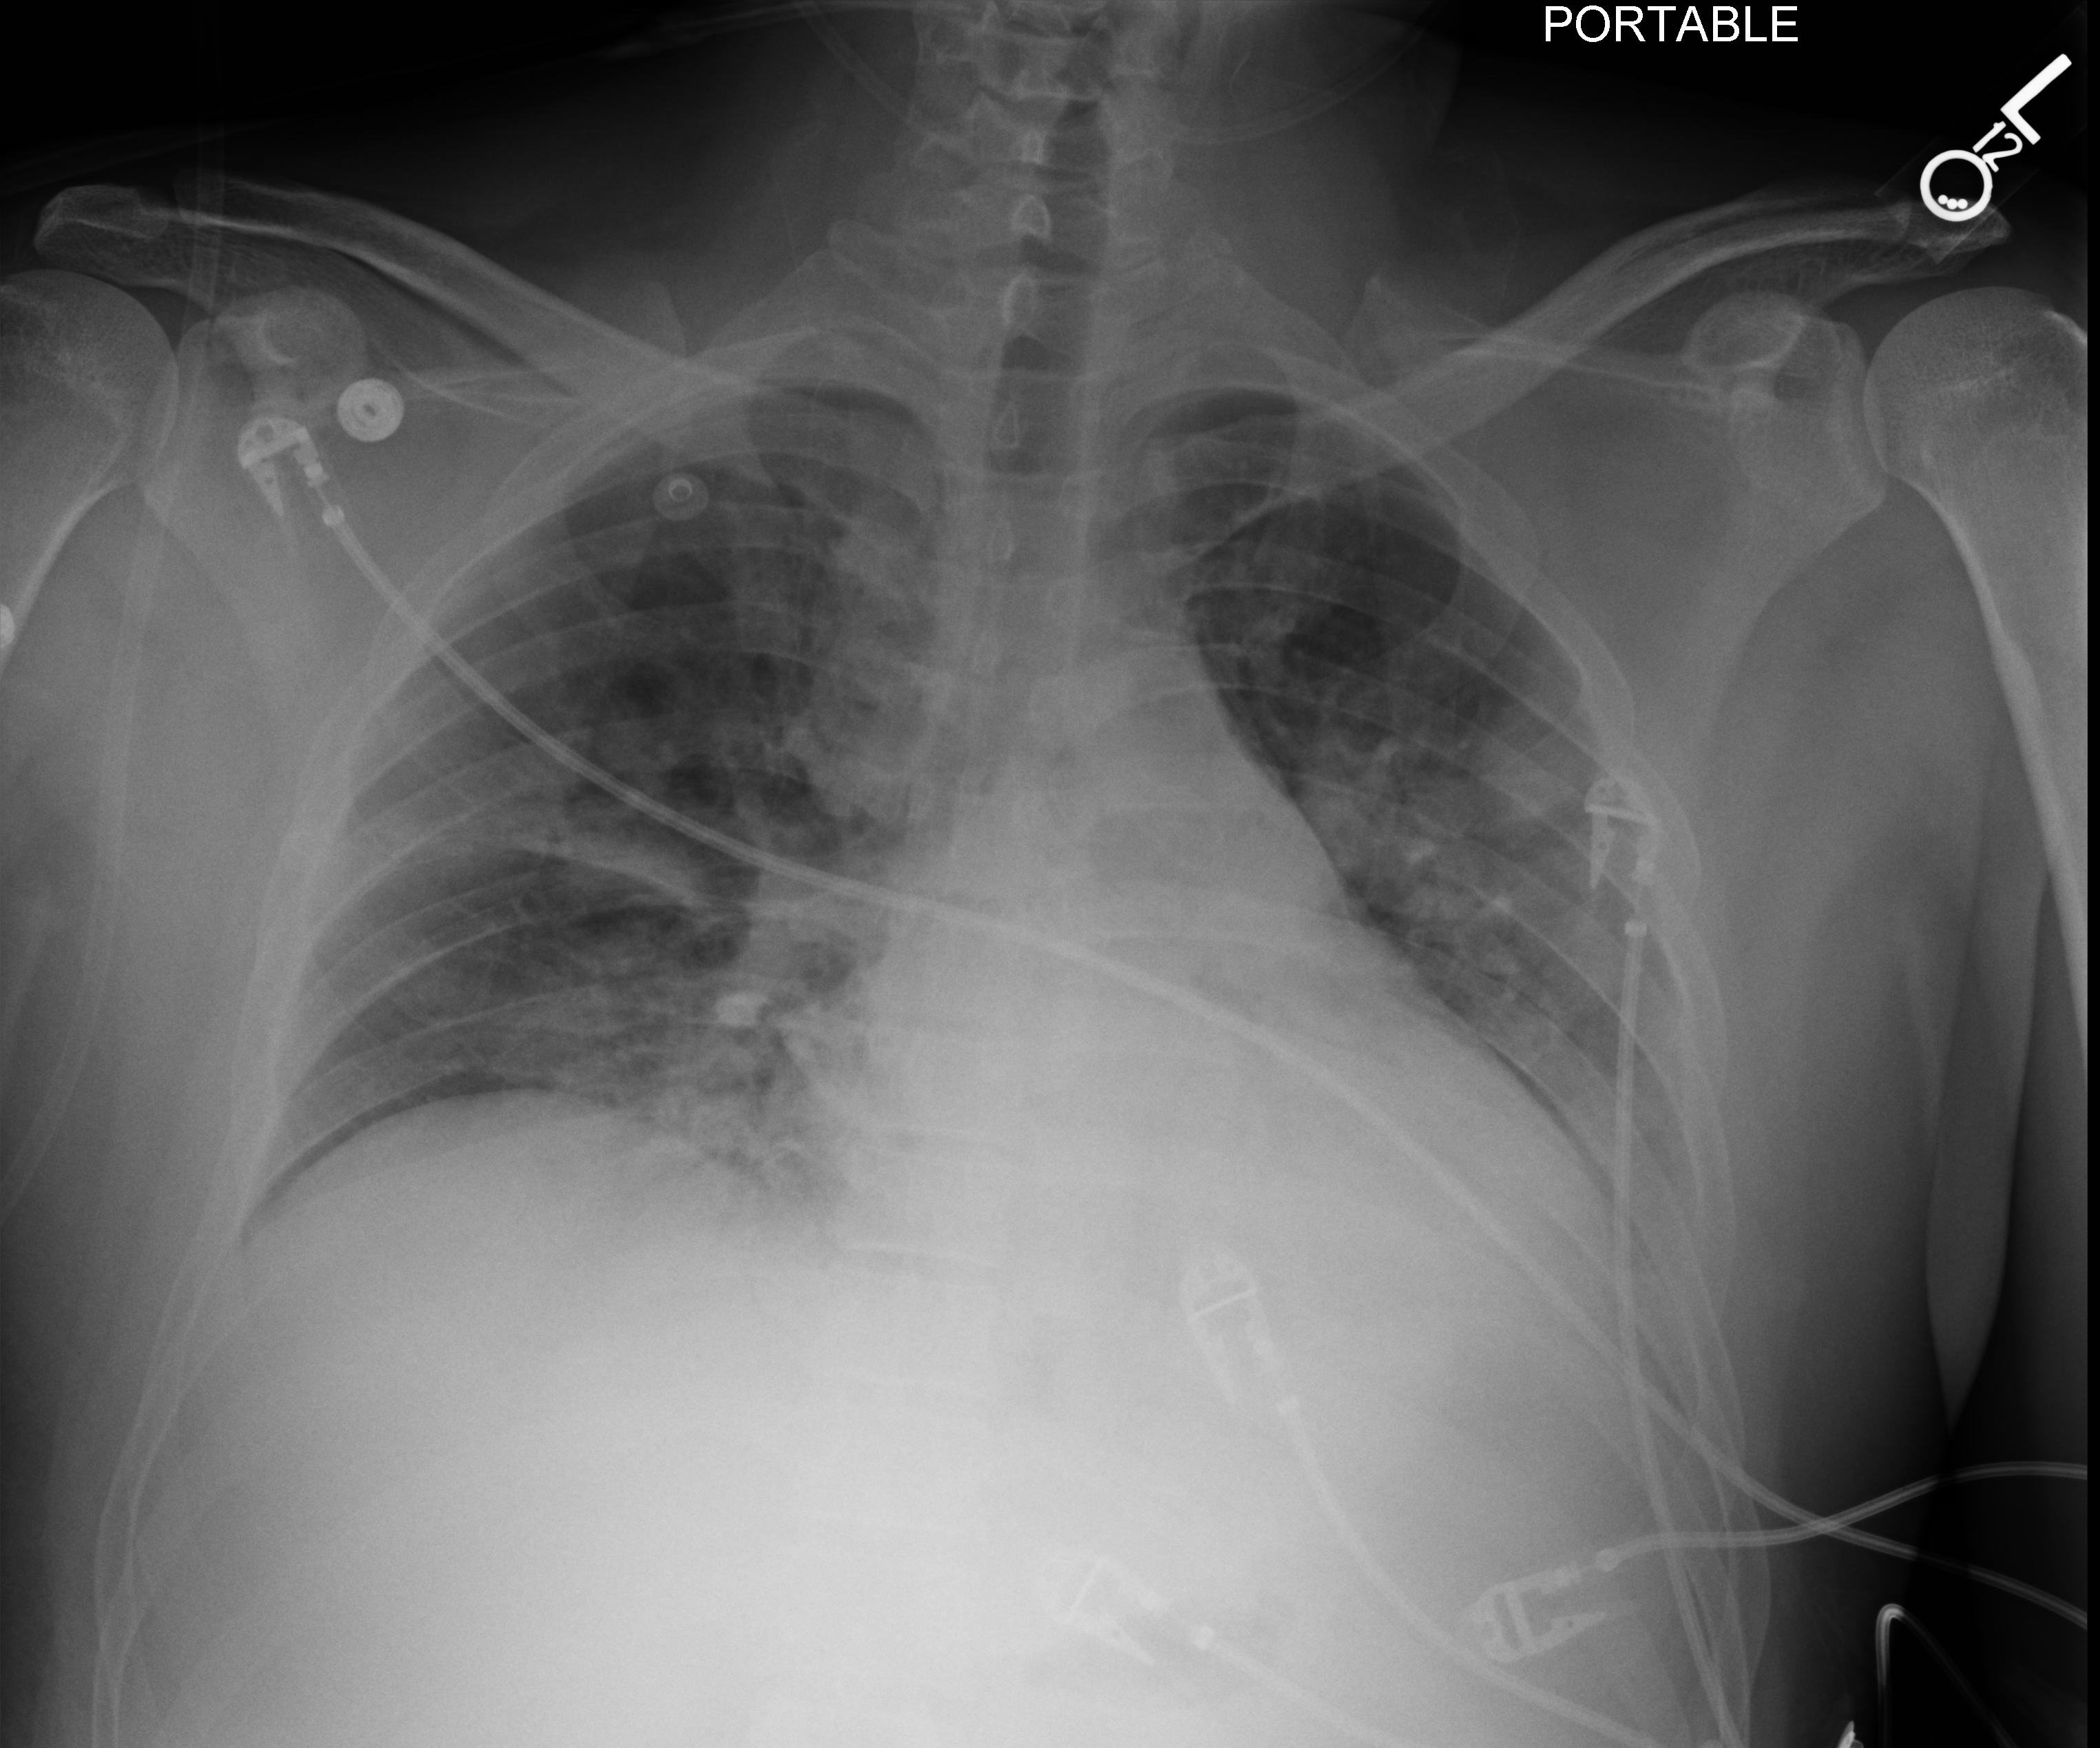
Portable chest radiograph, anteroposterior (AP) projection. Adult patient hospitalised with COVID-19, age 18–59 years.
Hospital-stay facts (about this admission, not read from this image; timing relative to this image not recorded): smoking status (admission record): never.